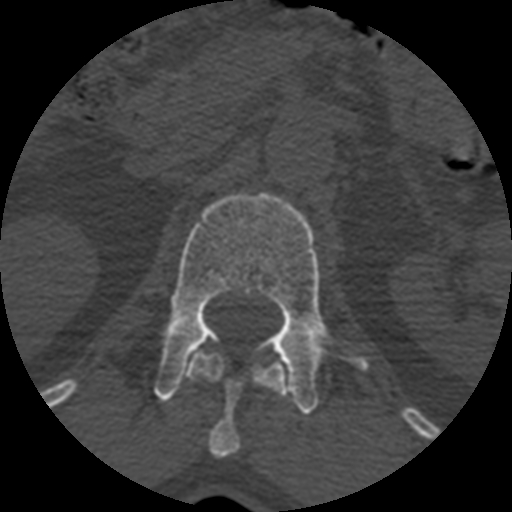
CT including the spine, one axial slice; slice 367 of 399 in the series (ordered by position); bone window (W 1800 / L 400 HU); 1.25 mm slice thickness; 512 × 512 image matrix, field of view 160 × 160 mm. Patient age 71 years. Case-level facts recorded for this patient, not image findings: primary cancer: prostate.
Outlined on this slice (semi-automatically segmented with operator editing):
- L1 vertebra: bounding box (x1, y1, x2, y2) in pixels: (155, 192, 370, 413)
- T12 vertebra: (185, 347, 287, 458)